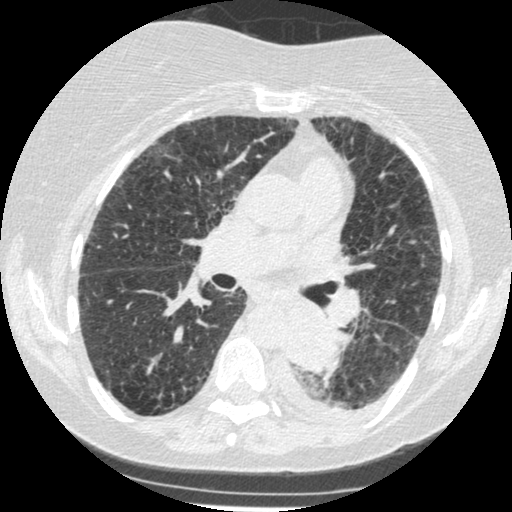
Low-dose screening chest CT, one axial slice. Position 142 of 341 along the scan axis. Reconstruction kernel STANDARD. Lung window (W 1500 / L -600 HU). 1.25 mm slice thickness. 512 × 512 image matrix.
Structures marked on this image (manually delineated by an expert):
- lesion 1 (tumor, lower lobe of left lung): bounding box [x1, y1, x2, y2] px = [285, 307, 337, 373]